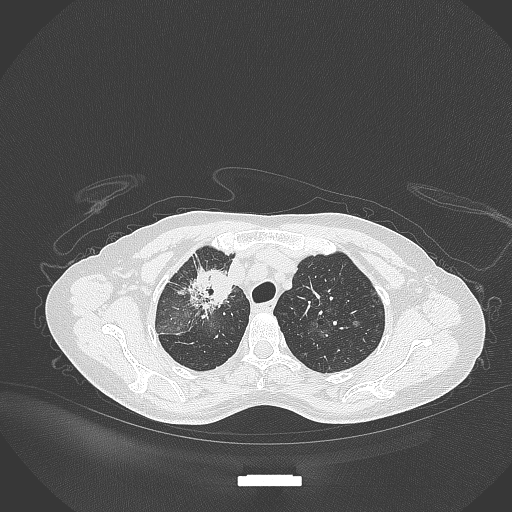
Chest CT, one axial slice. Slice 260 of 284 in the series (ordered by position). Reconstruction kernel B70f. 120 kVp. Lung window (W 1500 / L -600 HU). 1 mm slice thickness. 512 × 512 image matrix, field of view 400 × 400 mm. Patient: female, 59 years. From the clinical record (not read from this slice): clinical TNM (as recorded): T3 N0 M0; histopathological grade: G1.
Outlined on this slice (bounding box drawn by a radiologist):
- lung tumour (recorded histology: adenocarcinoma): bounding box (x1, y1, x2, y2) in pixels: (177, 262, 237, 311)